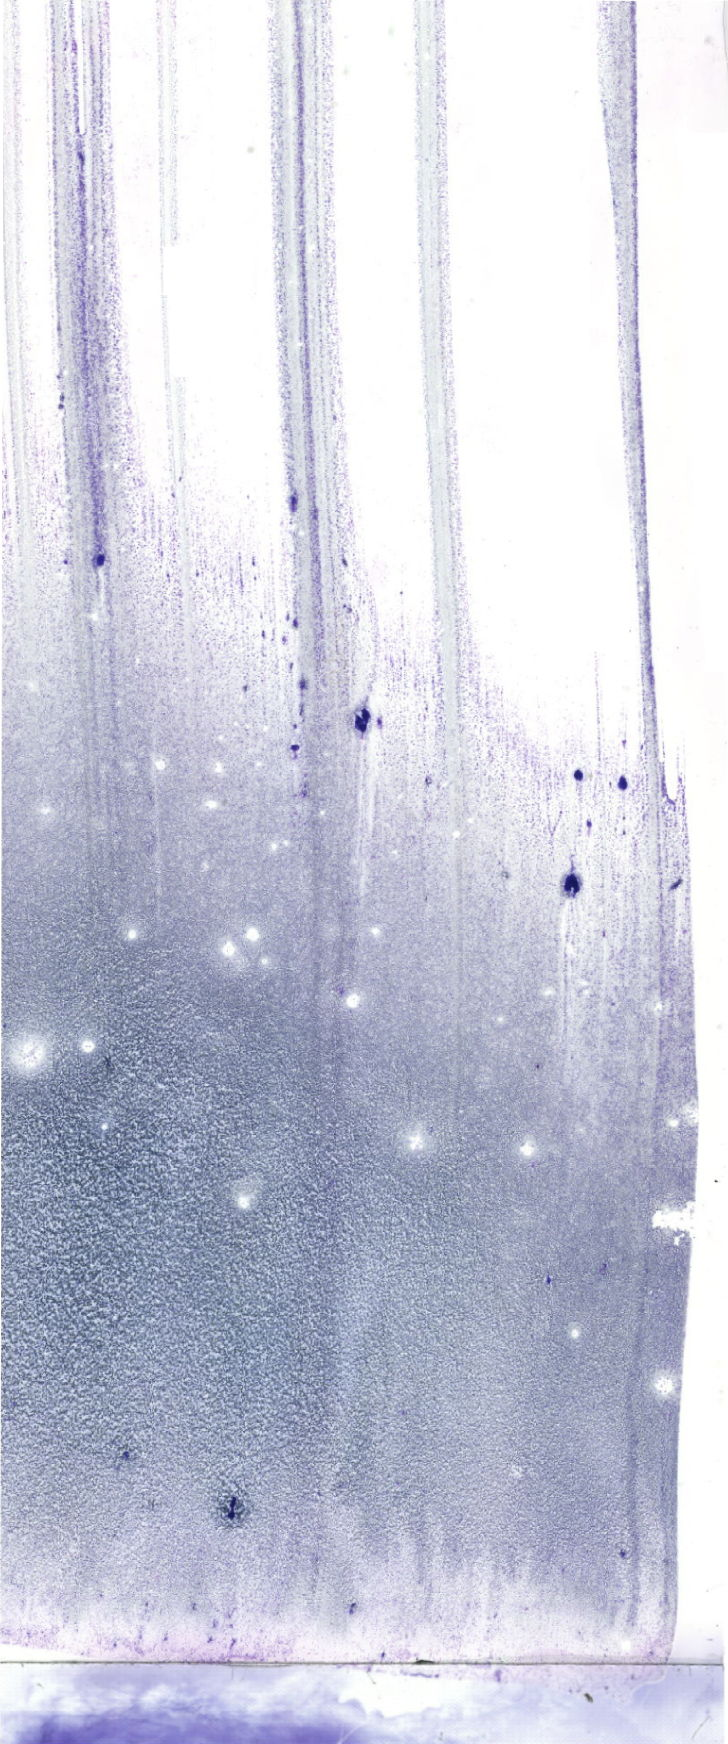
Bone marrow aspirate smear, May-Grünwald-Giemsa (MGG) stain, whole-slide image — shown as a low-resolution overview of the whole scanned area (about 20.6 x 49.4 mm). Patient sex: male.
Diagnosis: Acute Myelomonocytic Leukemia.